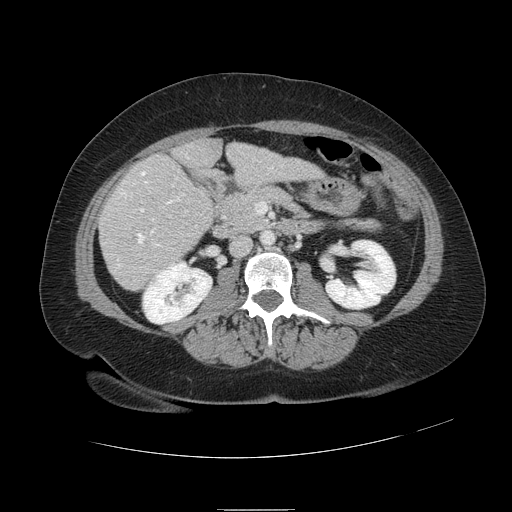
Contrast-enhanced abdominal CT, one axial slice; position 34 of 121 along the scan axis; 120 kVp; intravenous contrast given; soft-tissue window (W 400 / L 40 HU); 2.5 mm slice thickness; 512 × 512 image matrix, field of view 400 × 400 mm. Female patient, age 52 years. Case-level facts recorded for this patient, not image findings: diagnosis: colorectal cancer liver metastases, imaged before liver resection; multiple liver metastases: yes; largest metastasis: 6.3 cm; disease in both lobes: no.
Outlined on this slice (expert manual segmentation):
- hepatic veins: box from (x=118, y=172) to (x=177, y=267) px
- liver: (x=100, y=140)–(x=320, y=290)
- planned liver remnant (the part of the liver to remain after resection): (x=175, y=140)–(x=321, y=182)
- portal vein (with intrahepatic branches): (x=141, y=209)–(x=144, y=212)